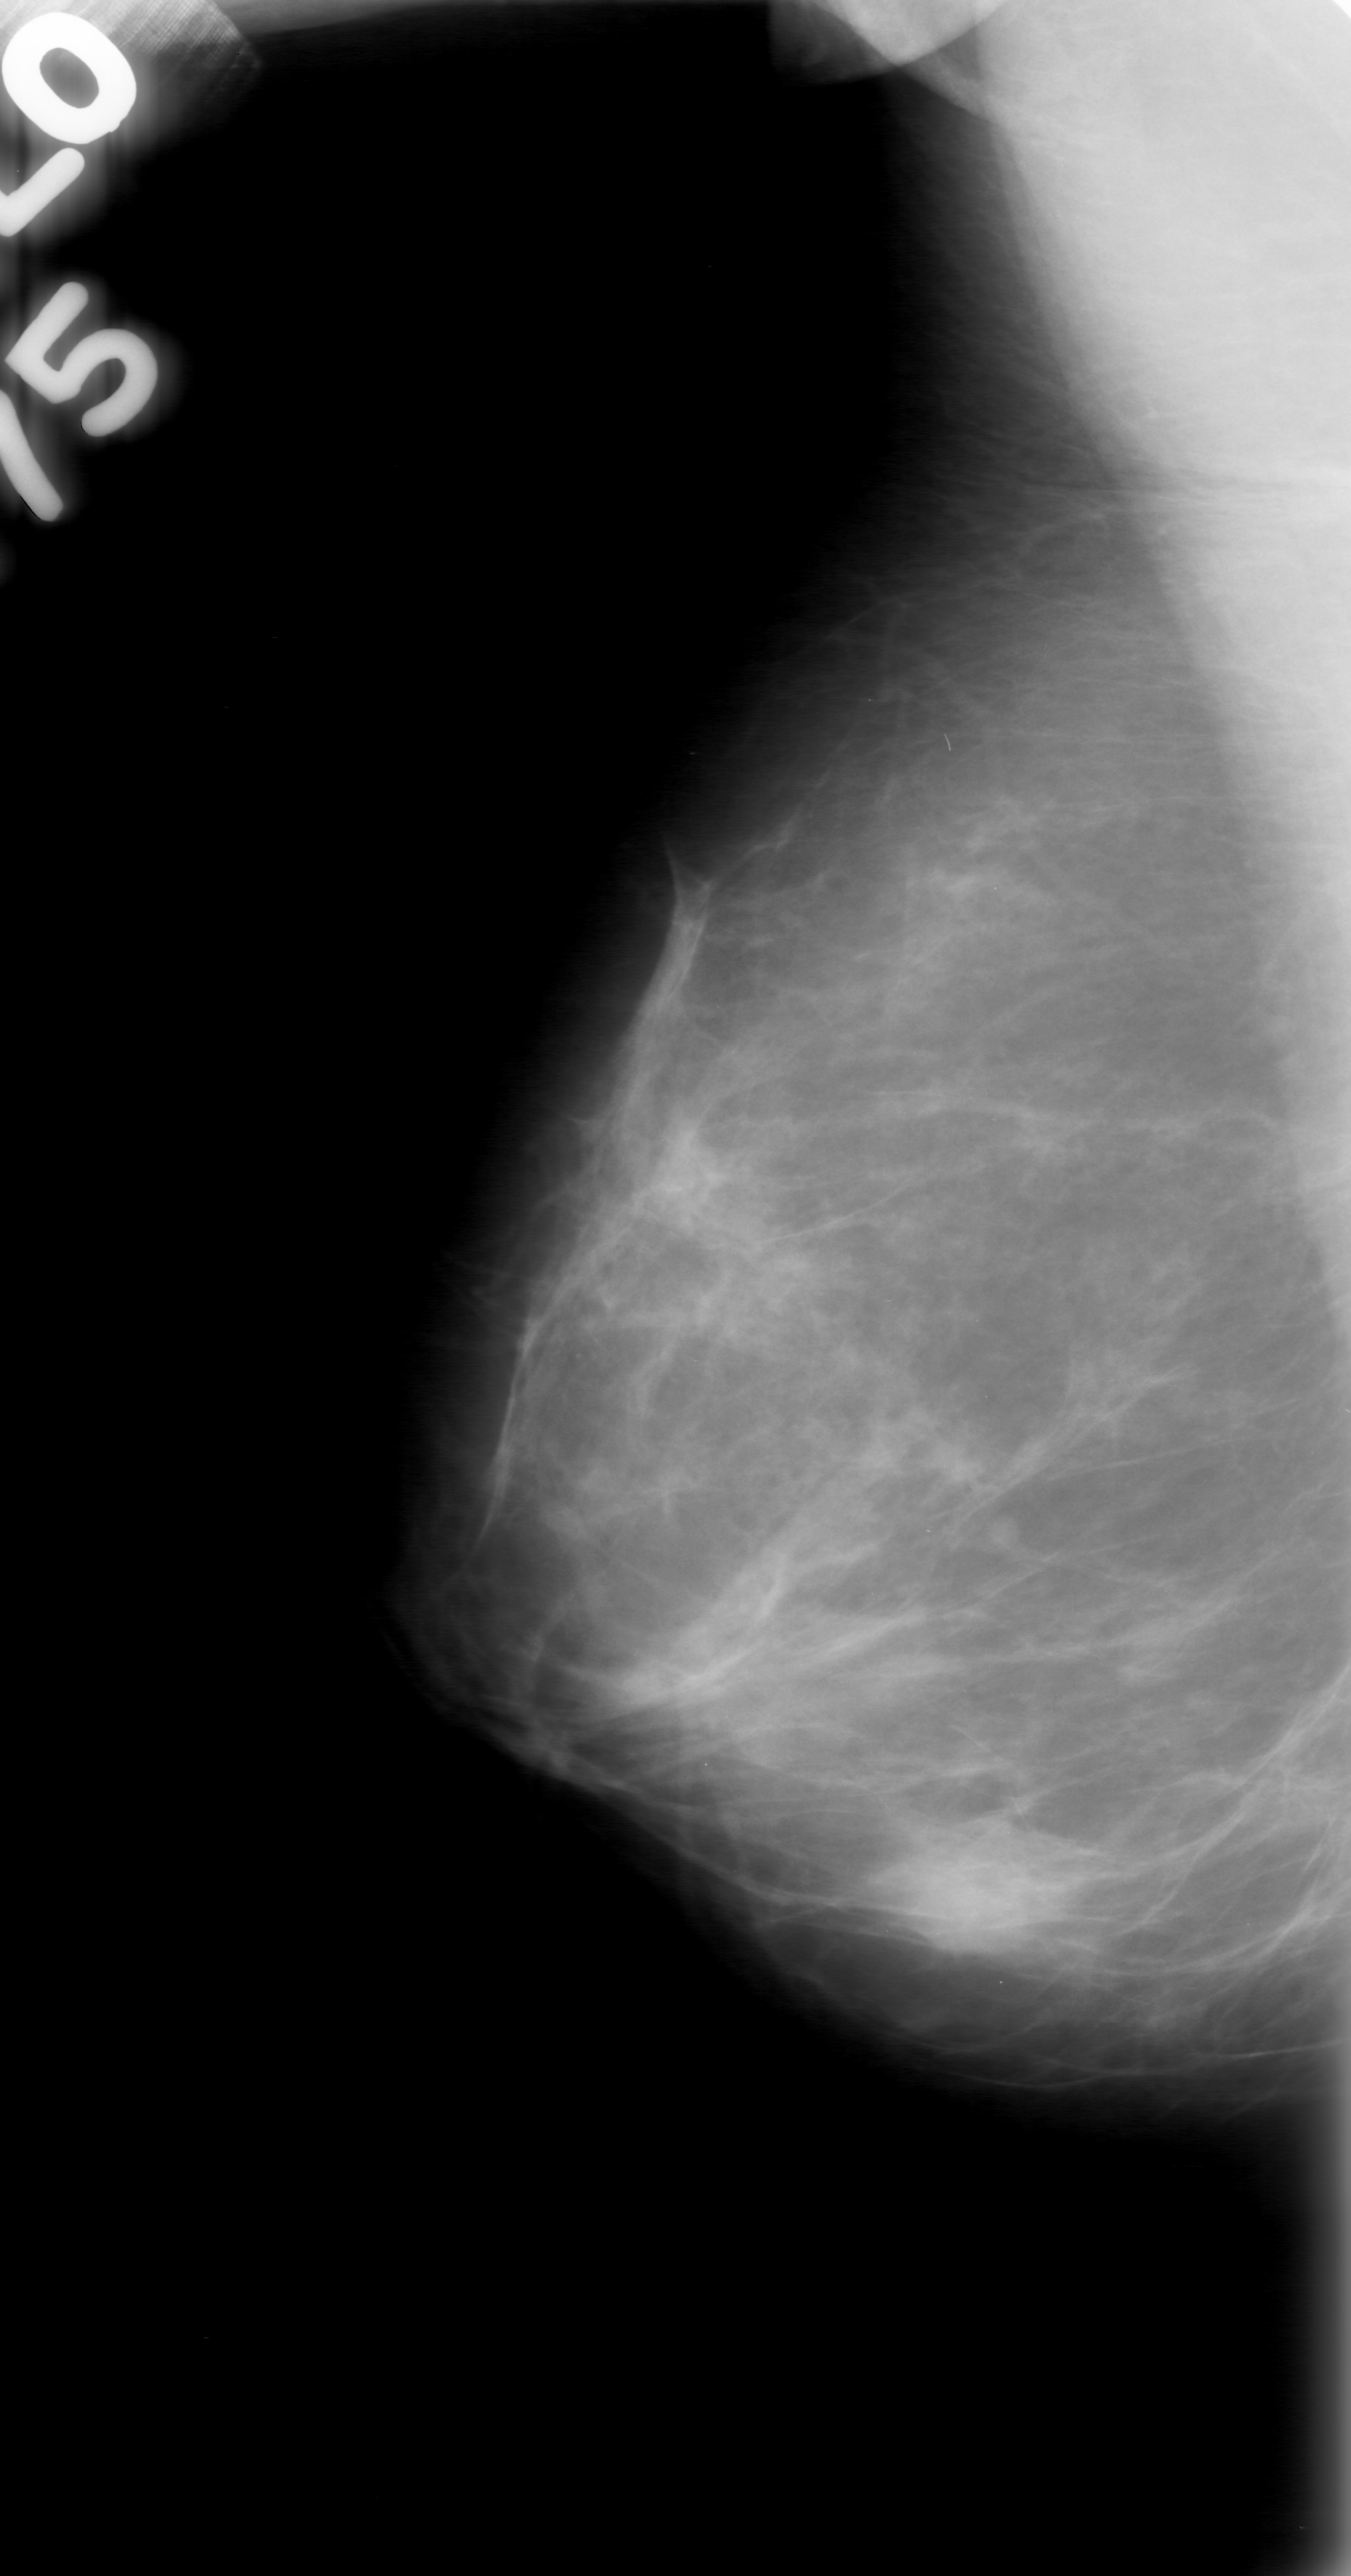
Mammogram (digitized film), right breast, MLO view.
Radiologist-marked abnormalities on this image: mass, shape oval, margins obscured; BI-RADS assessment category 0 (incomplete: needs additional imaging); pathology (as recorded): benign.